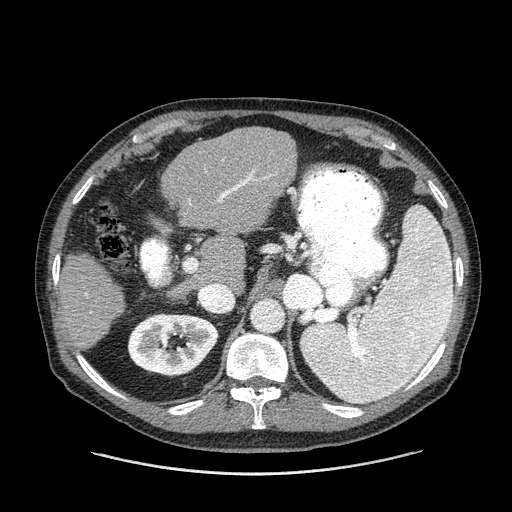
Contrast-enhanced abdominal CT (liver protocol), one axial slice. Slice 82 of 180 in the series (ordered by position). Reconstruction kernel STANDARD. 120 kVp. One of 2 acquisitions stored at this slice position. Soft-tissue window (W 400 / L 40 HU). 2.5 mm slice thickness. 512 × 512 image matrix, field of view 420 × 420 mm. Case-level facts recorded for this patient, not image findings: diagnosis: hepatocellular carcinoma (patient treated with transarterial chemoembolisation; whether this scan precedes or follows treatment is not stated here); TNM stage (as recorded): Stage-II; Child-Pugh class: A; tumour differentiation: well differentiated; tumour nodularity: multinodular.
Structures marked on this image (semi-automatic segmentation, software-assisted and operator-edited):
- liver parenchyma outside the tumour (the mass and vessels are separate outlines, so this box may not span the whole liver): bounding box [x1, y1, x2, y2] px = [54, 126, 296, 350]
- liver vessels: [56, 159, 272, 296]